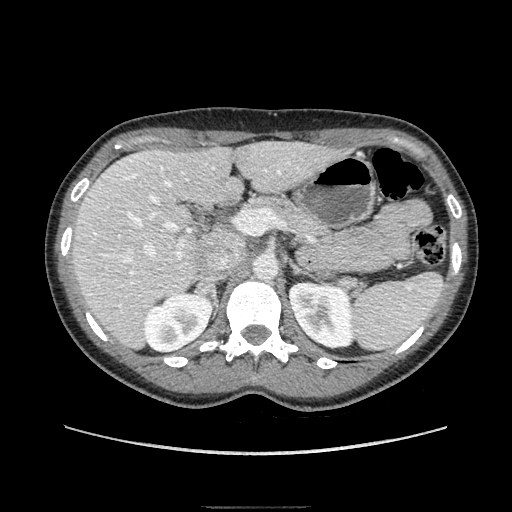
Contrast-enhanced abdominal CT, one axial slice. Slice 110 of 193 in the series (ordered by position). Soft-tissue window (W 400 / L 40 HU). 1.25 mm slice thickness. 512 × 512 image matrix, field of view 380 × 380 mm. Female patient. Case-level facts recorded for this patient, not image findings: diagnosis: adrenocortical carcinoma; tumour side: right adrenal; tumour size at pathology: 3 cm; Ki-67 index: 4 %; stage (as recorded): 1.
Outlined on this slice (semi-automatic segmentation, software-assisted and operator-edited):
- mass: box from (x=195, y=281) to (x=217, y=318) px